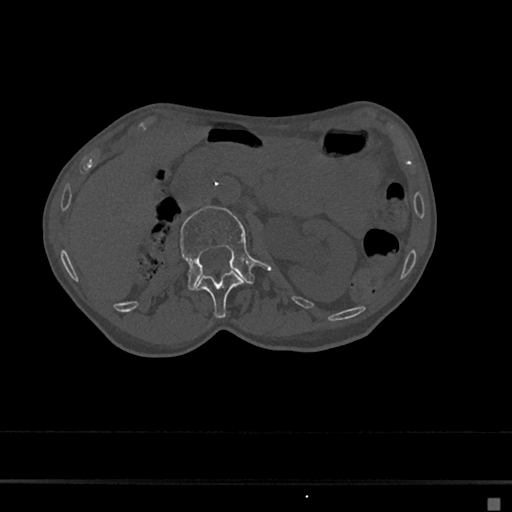
CT including the spine, one axial slice; reconstruction kernel Br40s/3; bone window (W 1800 / L 400 HU); 0.5 mm slice thickness; 512 × 512 image matrix. Patient: female, 68 years. From the clinical record (not read from this slice): primary cancer: renal.
Outlined on this slice (semi-automatic segmentation, software-assisted and operator-edited):
- L1 vertebra: bounding box (x1, y1, x2, y2) in pixels: (196, 270, 243, 319)
- L2 vertebra: (179, 206, 270, 290)